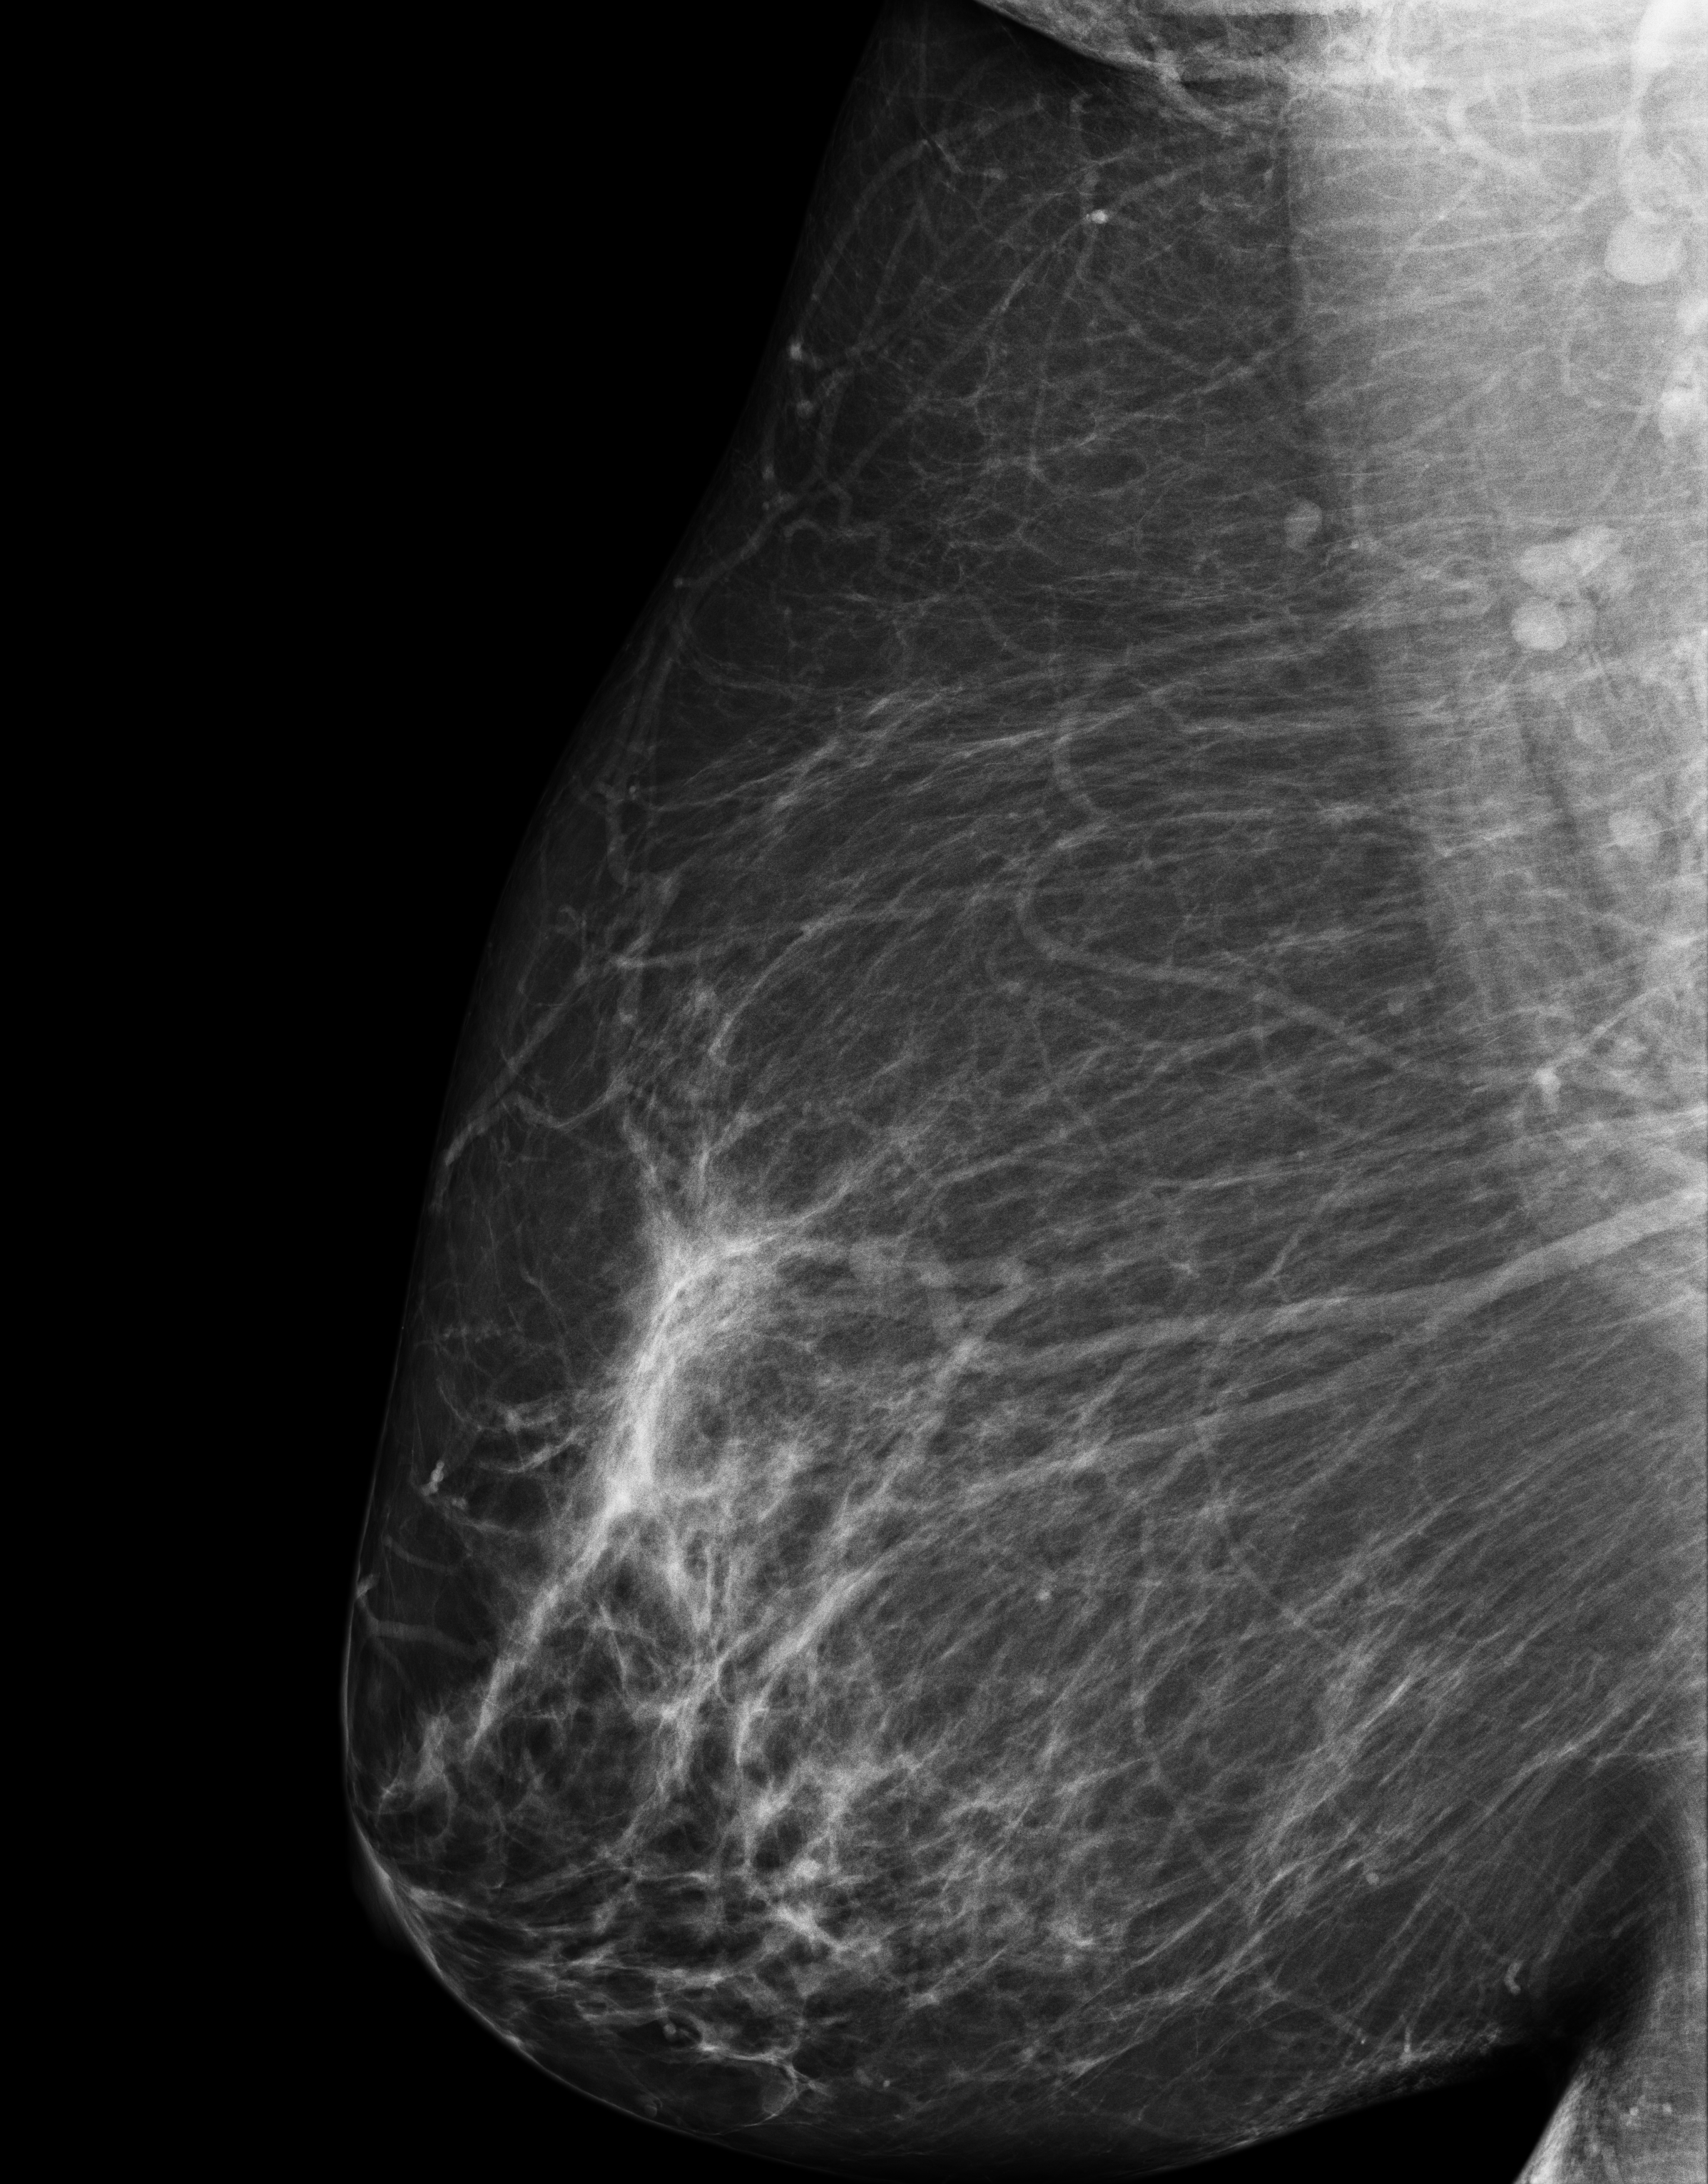
Screening examination. Patient: female, 58 years.
Image type: full-field digital mammogram. Breast: right. Projection: mediolateral oblique (MLO) view.